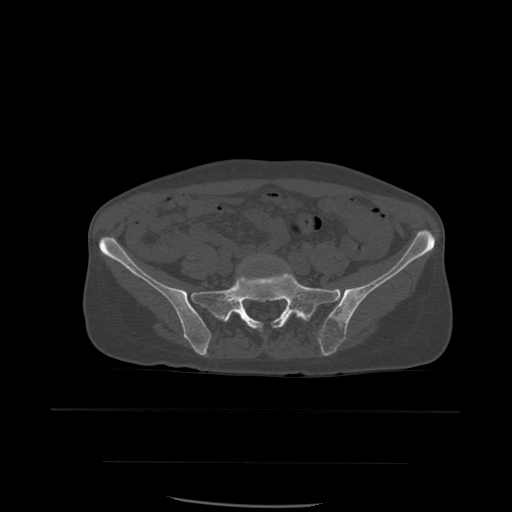
CT including the spine, one axial slice. Position 131 of 574 along the scan axis. Bone window (W 1800 / L 400 HU). 512 × 512 image matrix, field of view 392 × 392 mm. Patient age 48 years. Case-level facts recorded for this patient, not image findings: primary cancer: lung; vertebrae with lytic lesions (as recorded): T11.
Outlined on this slice (semi-automatically segmented with operator editing):
- L5 vertebra: bounding box <229,255,303,319> (left, top, right, bottom; pixels)